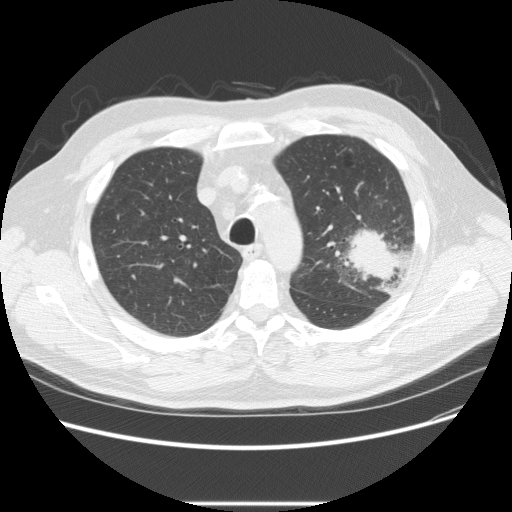
Low-dose screening chest CT, one axial slice. Position 173 of 233 along the scan axis. 120 kVp. Lung window (W 1500 / L -600 HU). 2.5 mm slice thickness. 512 × 512 image matrix, field of view 380 × 380 mm.
Outlined on this slice (manually delineated by an expert):
- lesion 1 (tumor, upper lobe of left lung): bounding box <344,225,407,284> (left, top, right, bottom; pixels)